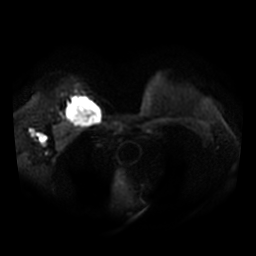
Breast MRI, one axial slice. Slice 27 of 36 in the series (ordered by position). Diffusion-weighted series; image 2 of 4 stored at this slice position (different b-values; order by instance number). 3 T. 256 × 256 image matrix, field of view 340 × 340 mm. Female patient.
Outlined on this slice (outlined manually by an expert reader):
- tumour on diffusion-weighted imaging: bounding box [x1, y1, x2, y2] px = [65, 97, 99, 125]